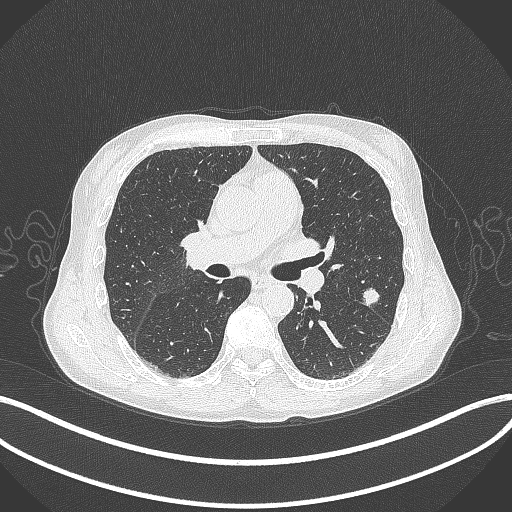
Chest CT, one axial slice; position 206 of 429 along the scan axis; 120 kVp; lung window (W 1500 / L -600 HU); 1 mm slice thickness; 512 × 512 image matrix. Male patient, age 58 years. Case-level facts recorded for this patient, not image findings: clinical TNM (as recorded): T1c N0 M0.
Annotated regions visible in this slice (rectangle marked by the reading radiologist):
- lung tumour (recorded histology: adenocarcinoma): bounding box (x1, y1, x2, y2) in pixels: (361, 285, 384, 304)